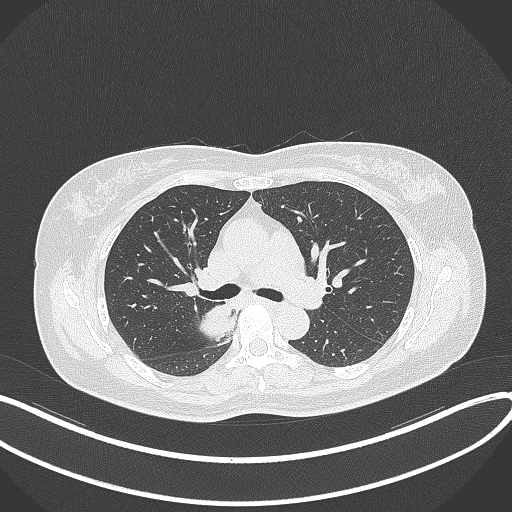
Chest CT, one axial slice. Slice 230 of 331 in the series (ordered by position). Reconstruction kernel B70f. 120 kVp. Lung window (W 1500 / L -600 HU). 512 × 512 image matrix. Patient: female, 54 years. Case-level facts recorded for this patient, not image findings: clinical TNM (as recorded): T4 N0 M0.
Structures marked on this image (bounding box drawn by a radiologist):
- lung tumour (recorded histology: adenocarcinoma): bounding box (x1, y1, x2, y2) in pixels: (198, 300, 240, 342)